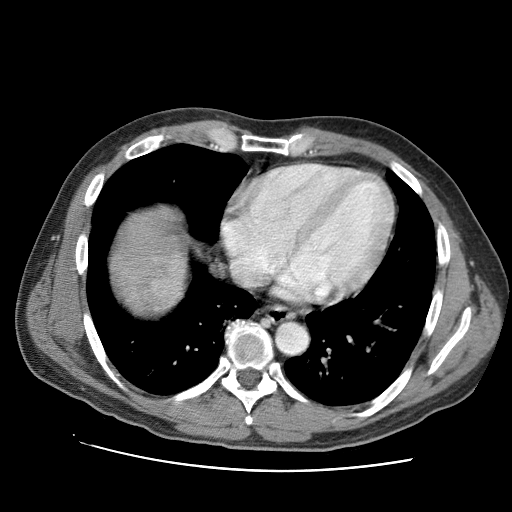
Contrast-enhanced abdominal CT (liver protocol), one axial slice; position 90 of 95 along the scan axis; reconstruction kernel STANDARD; one of 2 acquisitions stored at this slice position; soft-tissue window (W 400 / L 40 HU); 2.5 mm slice thickness; 512 × 512 image matrix, field of view 360 × 360 mm. Case-level facts recorded for this patient, not image findings: diagnosis: hepatocellular carcinoma (patient treated with transarterial chemoembolisation; whether this scan precedes or follows treatment is not stated here); TNM stage (as recorded): Stage-IVA; Child-Pugh class: A; tumour differentiation: moderately differentiated; tumour nodularity: multinodular.
Annotated regions visible in this slice (semi-automatically segmented with operator editing):
- liver parenchyma outside the tumour (the mass and vessels are separate outlines, so this box may not span the whole liver): bounding box [x1, y1, x2, y2] px = [110, 206, 186, 312]
- mass: [150, 255, 184, 307]